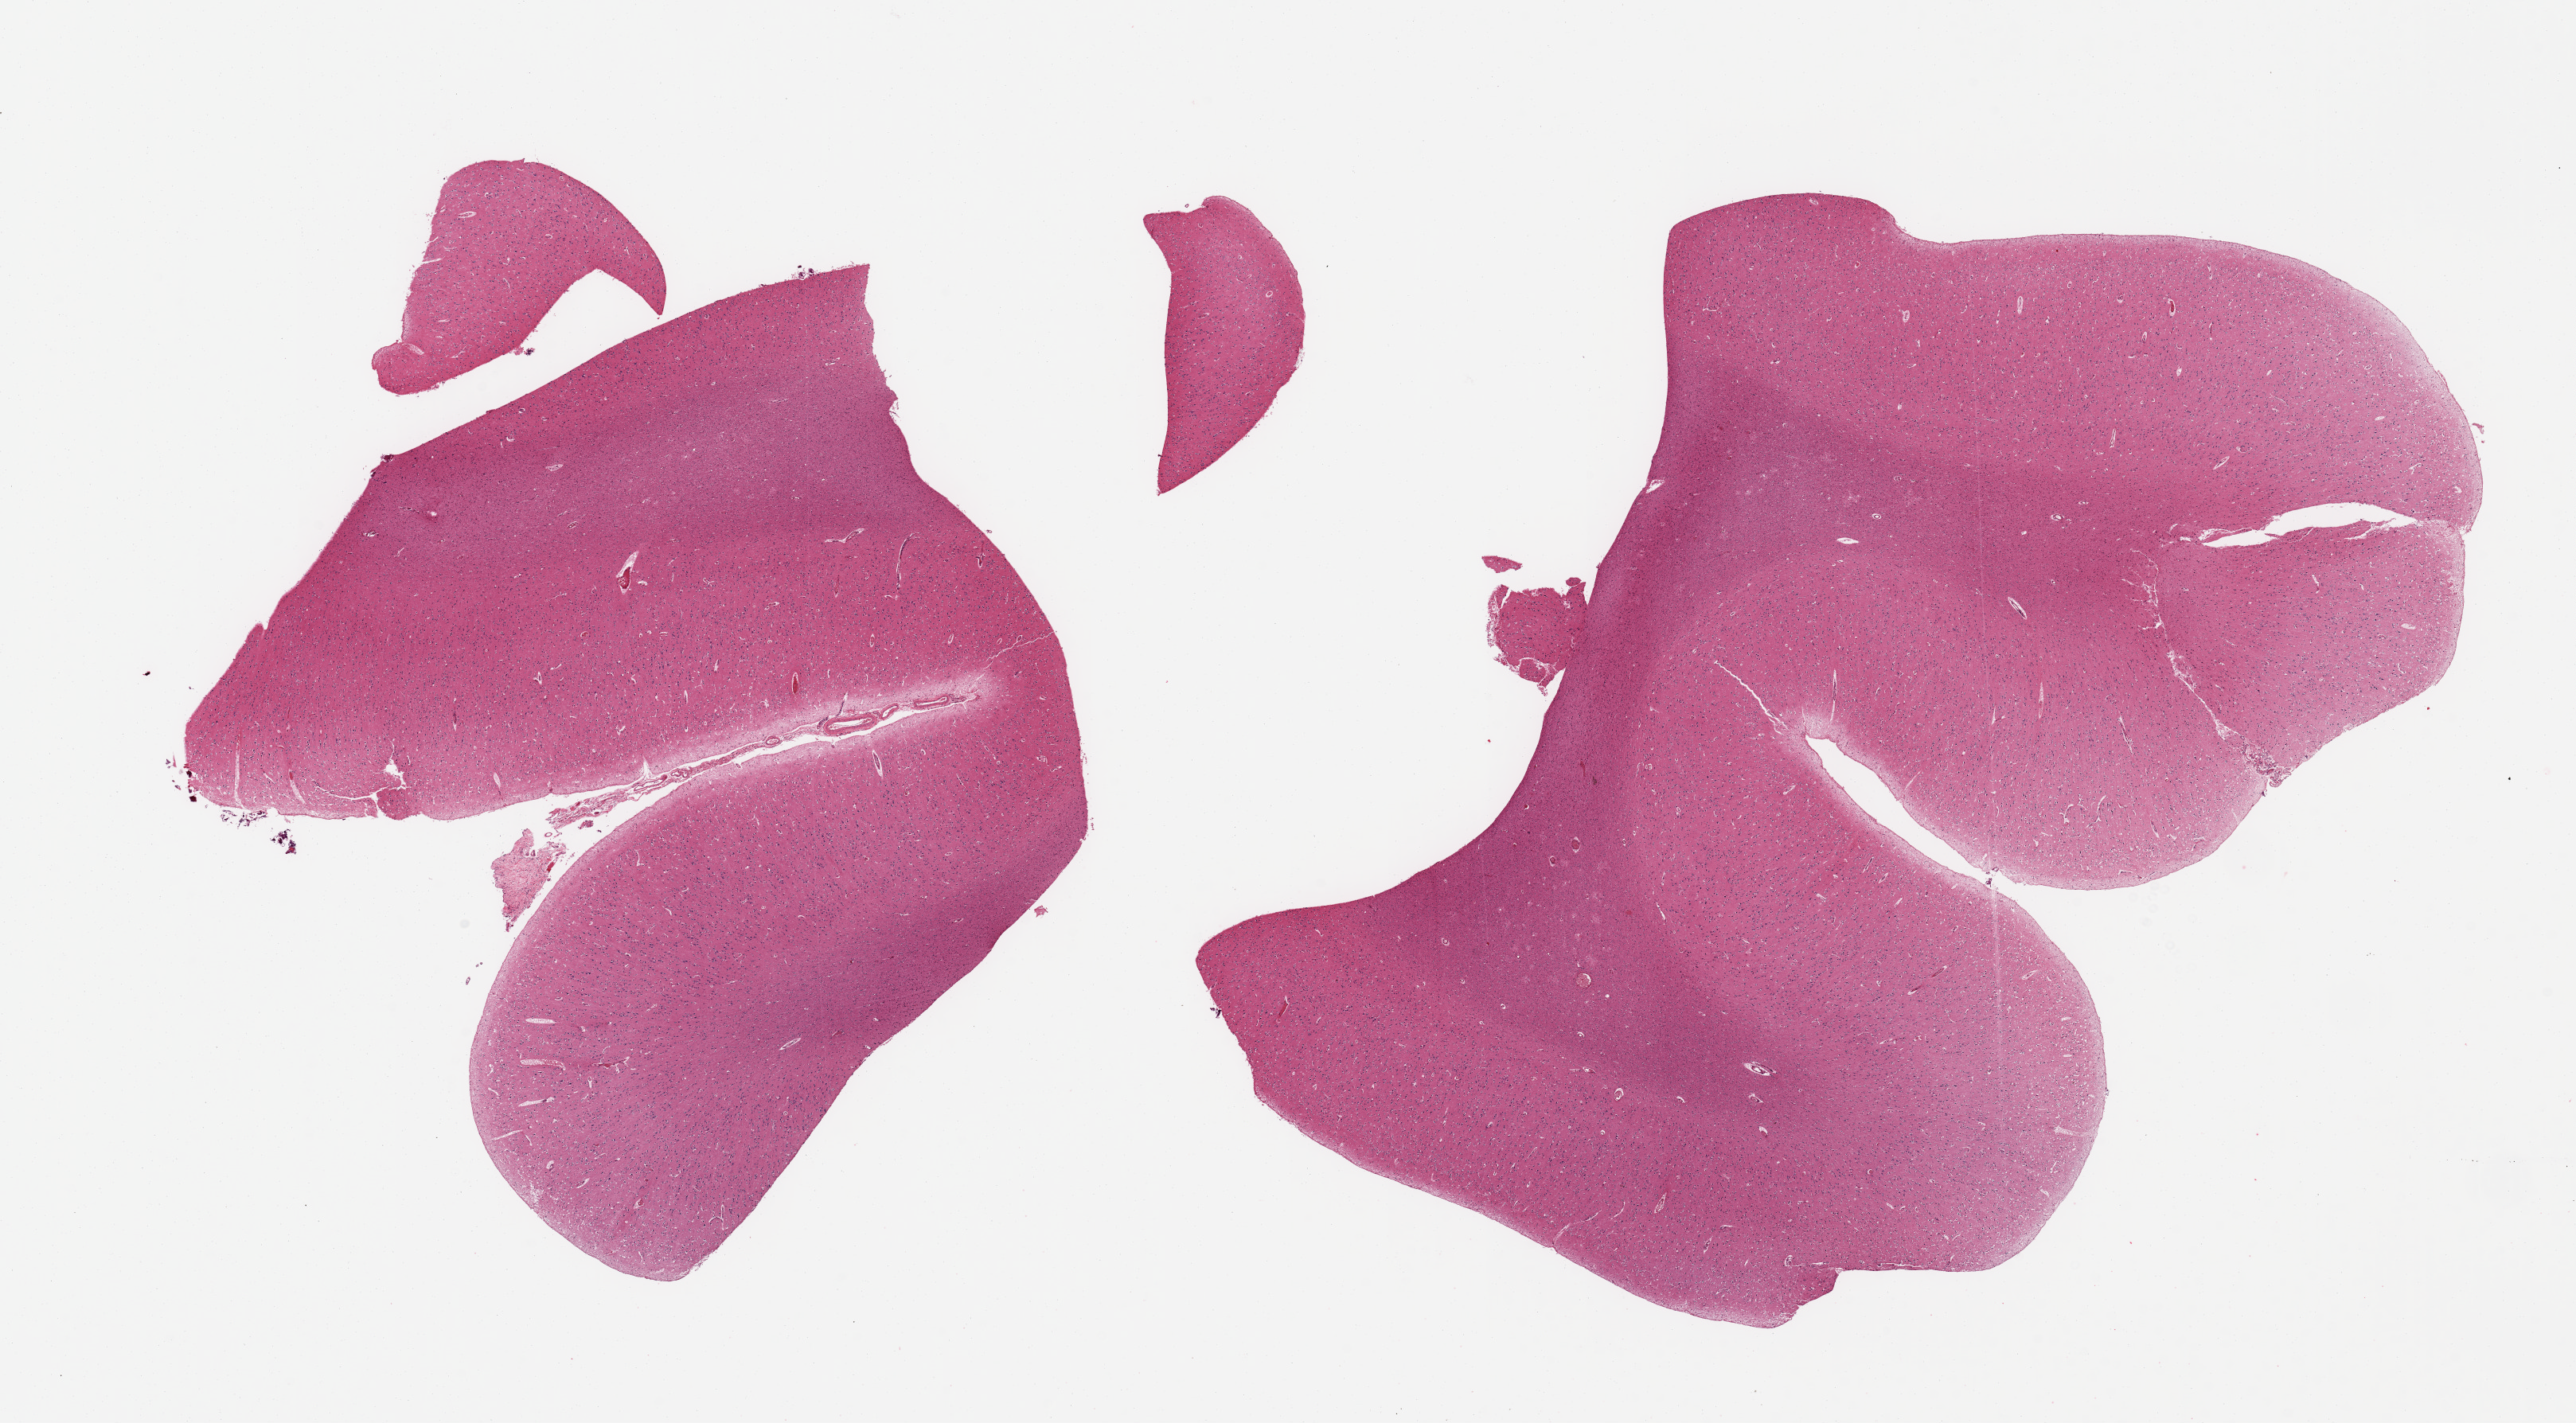
Digitized hematoxylin and eosin (H&E)-stained section, whole scanned area (about 25.6 x 14.1 mm) shown as a low-resolution overview, PAXgene-fixed, paraffin-embedded tissue, section of cerebral cortex (target tissue), donor tissue sample. Donor sex: male.
* pathologist's review note for this sample: 2 pieces, no abnormalities